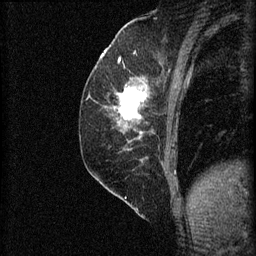
Breast MRI (dynamic contrast-enhanced), one sagittal slice; slice 26 of 60 in the series (ordered by position); 3 images stored at this slice position (order not interpretable as contrast timing); 1.5 T; TE 4.2 ms, TR 8.2 ms; 256 × 256 image matrix. Female patient, age 59 years.
Annotated regions visible in this slice (semi-automatic segmentation, software-assisted and operator-edited):
- analysis volume of interest (the breast-tissue region the enhancement analysis was run in; not a lesion): bounding box <92,74,152,131> (left, top, right, bottom; pixels)
- tumour enhancement mask (voxels above the 70 % enhancement threshold inside the analysis volume of interest): <114,82,148,121>